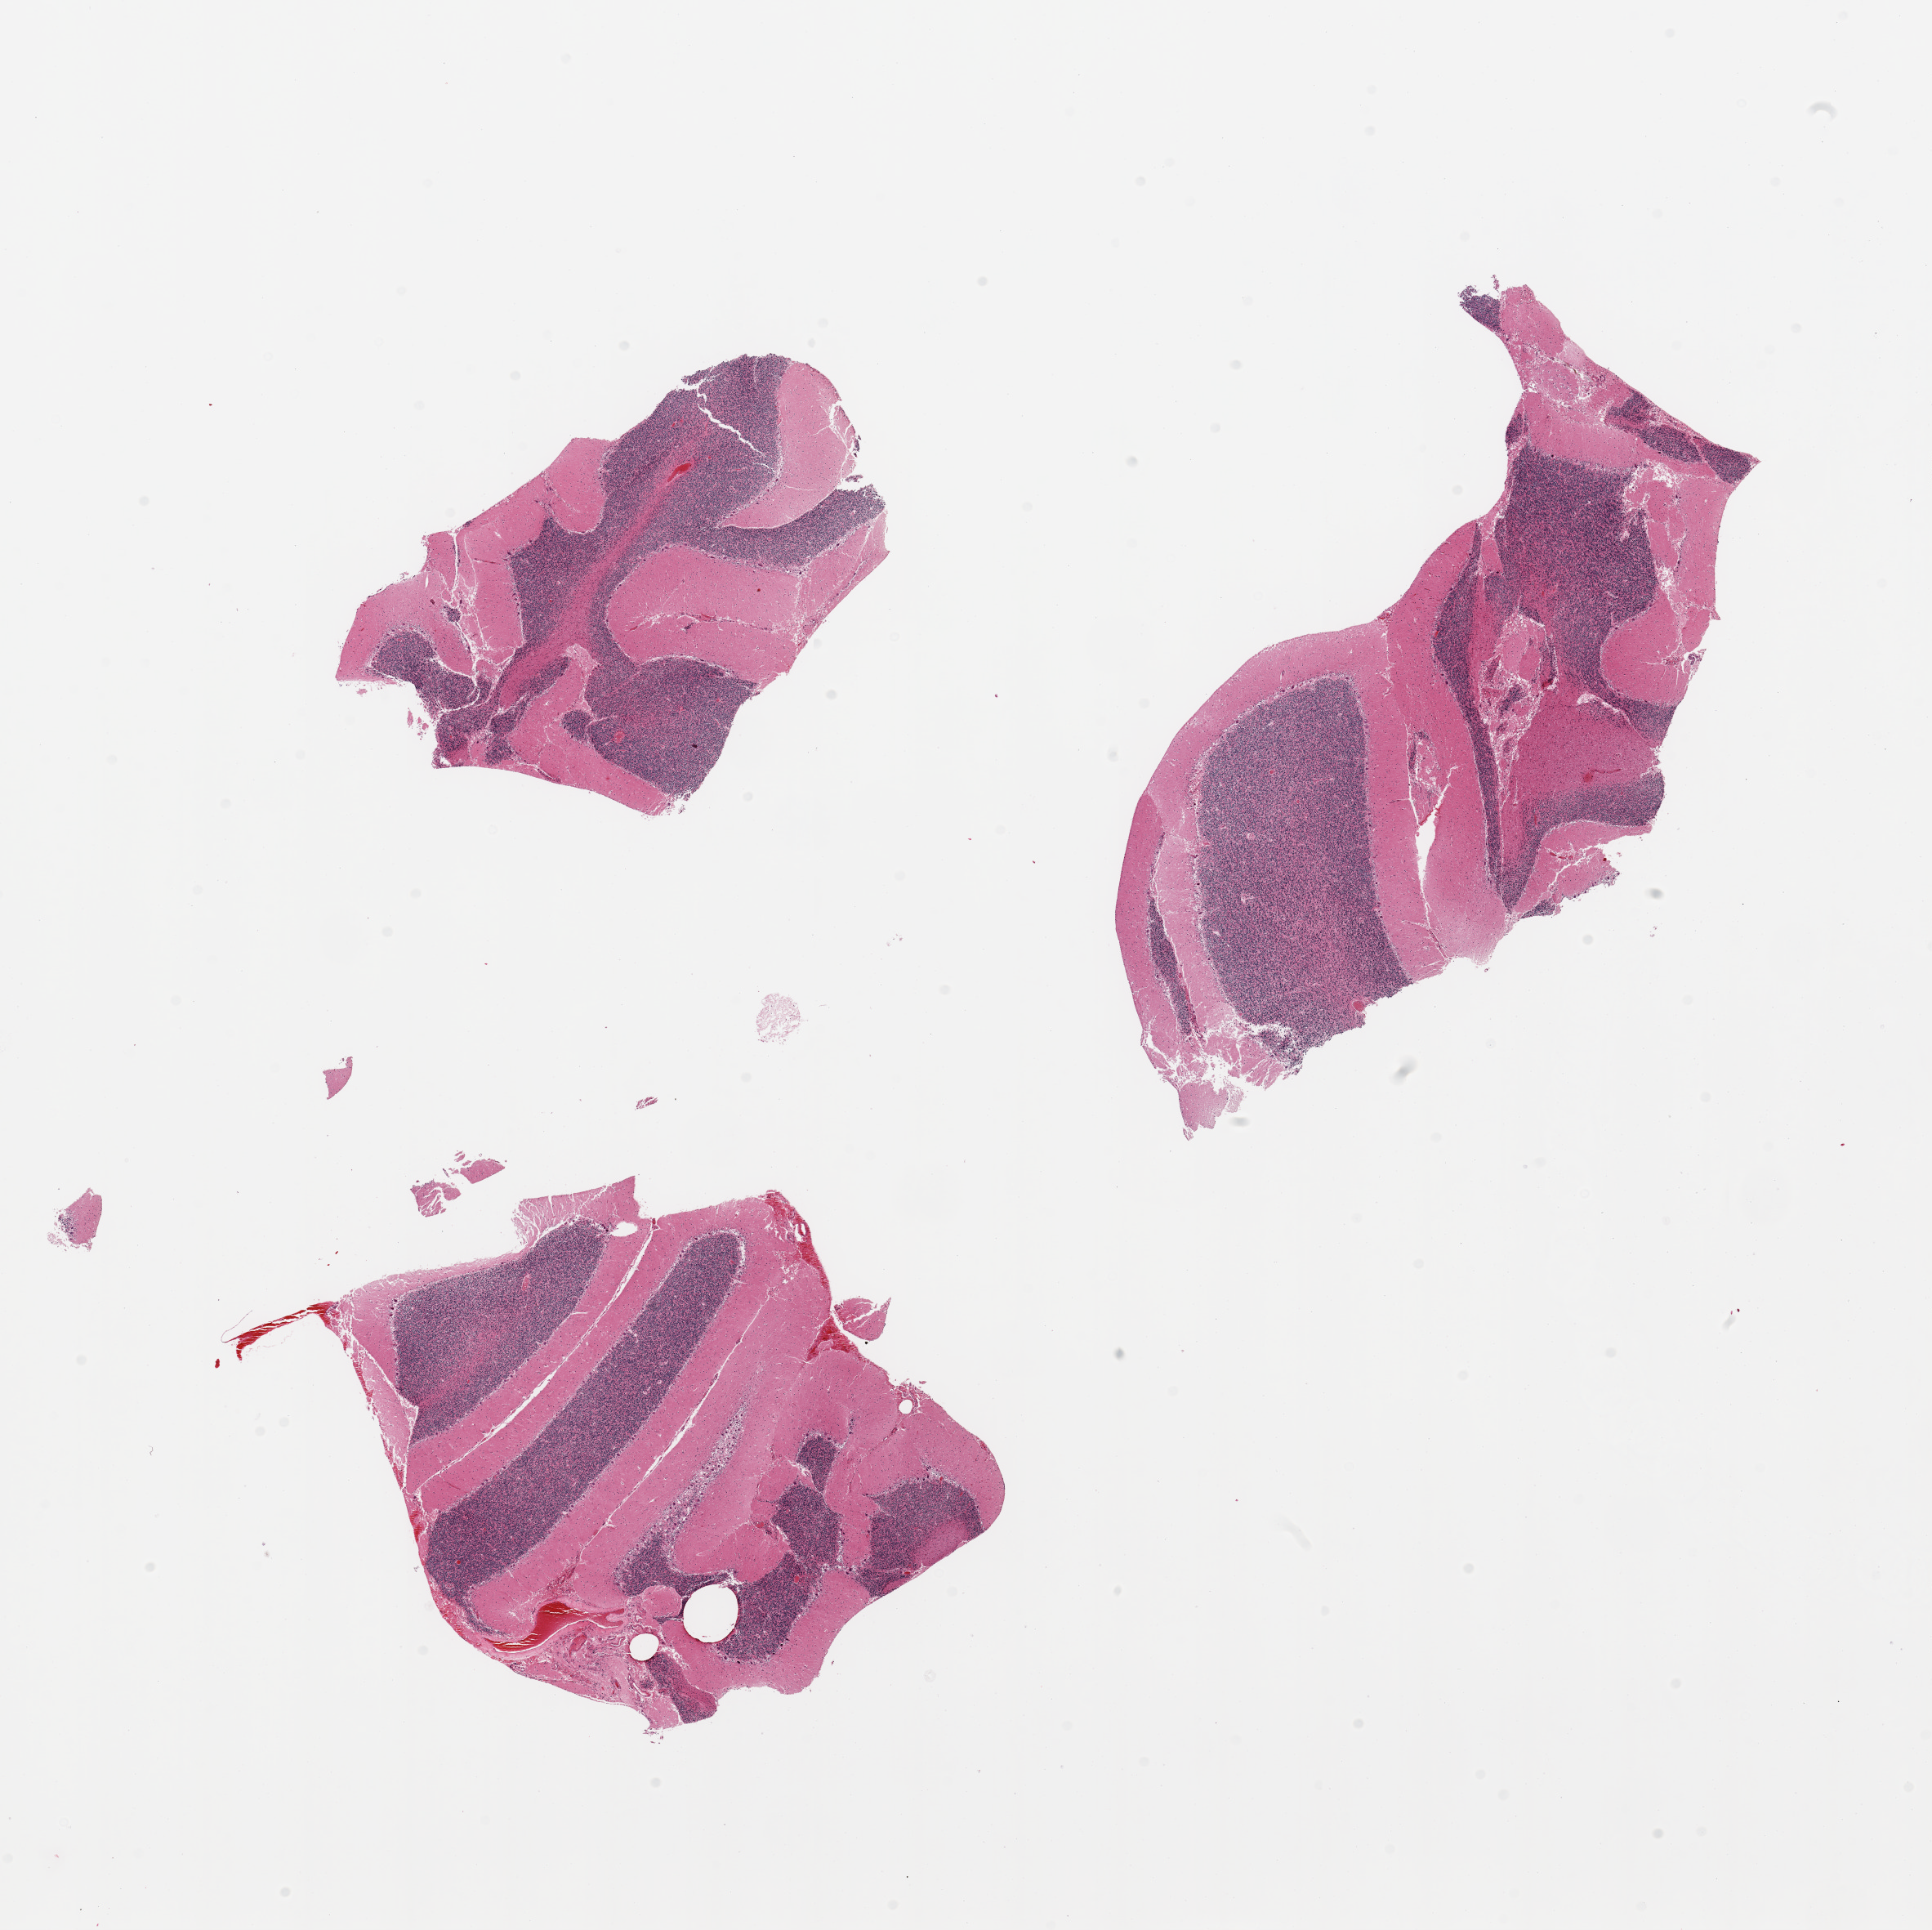
Haematoxylin and eosin whole-slide image, shown as a low-resolution overview of the whole scanned area (about 18.7 x 18.7 mm); PAXgene-fixed, paraffin-embedded tissue; sampled site (target tissue): cerebellum; donor tissue sample. Donor sex: male.
Reviewer comment on this tissue sample: 4 pieces, no abnormalities.